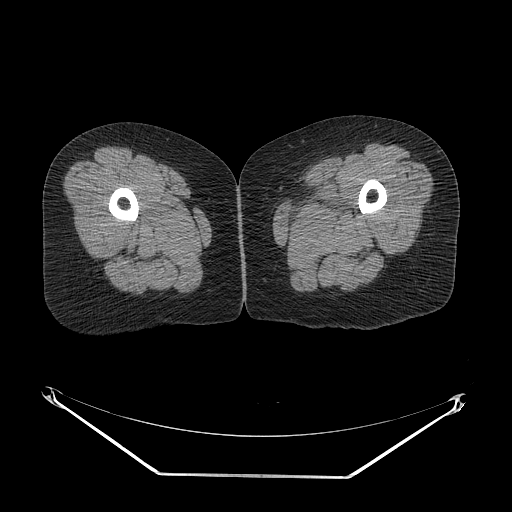
CT of an extremity soft-tissue mass (from a PET/CT study), one axial slice. Position 2 of 267 along the scan axis. 140 kVp. Soft-tissue window (W 400 / L 40 HU). 3.75 mm slice thickness. 512 × 512 image matrix. Female patient. Case-level facts recorded for this patient, not image findings: histological type: myxofibrosarcoma; grade: intermediate; site of the primary tumour: left thigh.
Structures marked on this image (expert contour drawn on MRI and transferred to this co-registered scan by the dataset authors):
- gross tumour volume including surrounding oedema: box from (x=292, y=206) to (x=346, y=231) px